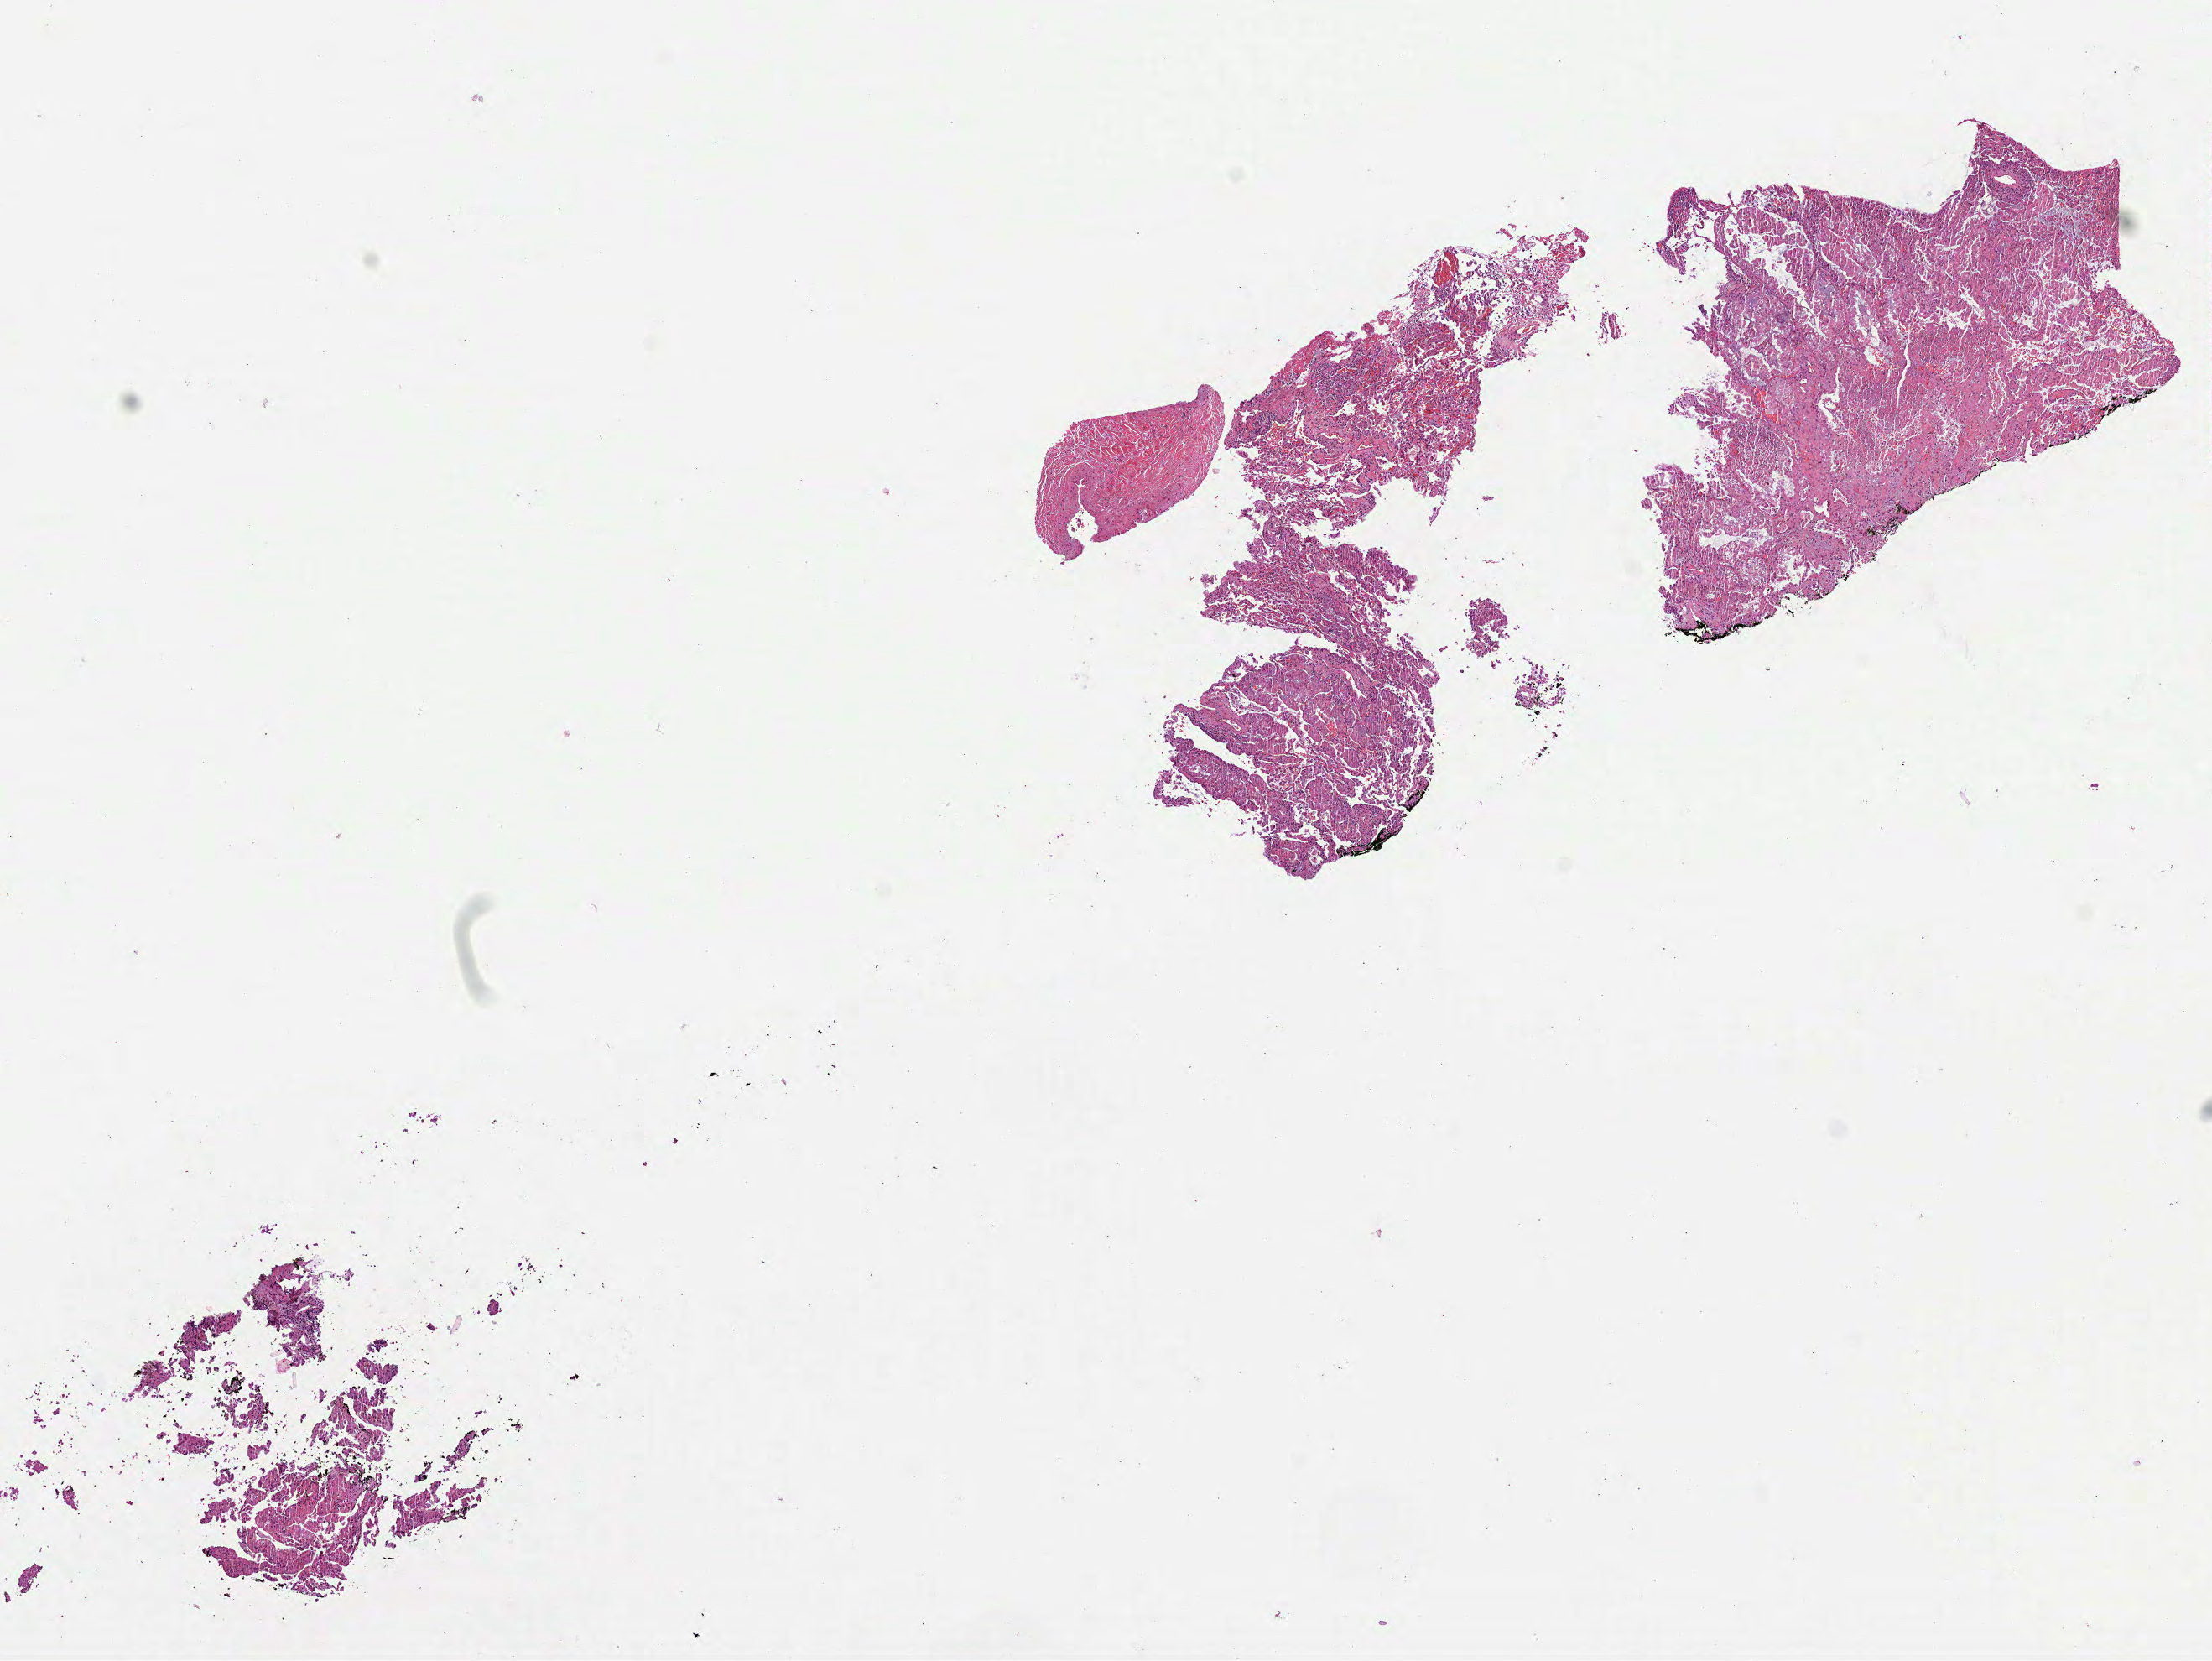
Digitized H&E-stained tissue section (whole slide), shown as a low-resolution overview of the whole scanned area (about 10.6 x 8.0 mm, from a 40x scan); FFPE section; lung, primary tumour sample. Male patient; age at initial diagnosis 62 years.
Histologic diagnosis: Adenocarcinoma, NOS (lower lobe, lung). AJCC pathologic stage: IIIA (7th edition).